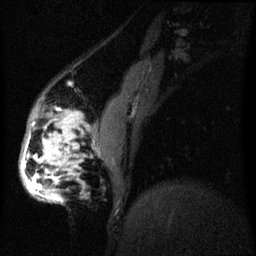
Breast MRI (dynamic contrast-enhanced), one sagittal slice; position 14 of 60 along the scan axis; dynamic contrast-enhanced series, image 2 of 3 at this slice position (ordered by acquisition); 1.5 T; TE 4.2 ms, TR 8 ms; 2.2 mm slice thickness; 256 × 256 image matrix. Female patient, age 50 years.
Outlined on this slice (semi-automatic segmentation, software-assisted and operator-edited):
- analysis volume of interest (the breast-tissue region the enhancement analysis was run in; not a lesion): bounding box (x1, y1, x2, y2) in pixels: (19, 112, 85, 205)
- tumour enhancement mask (voxels above the 70 % enhancement threshold inside the analysis volume of interest): (22, 118, 71, 197)